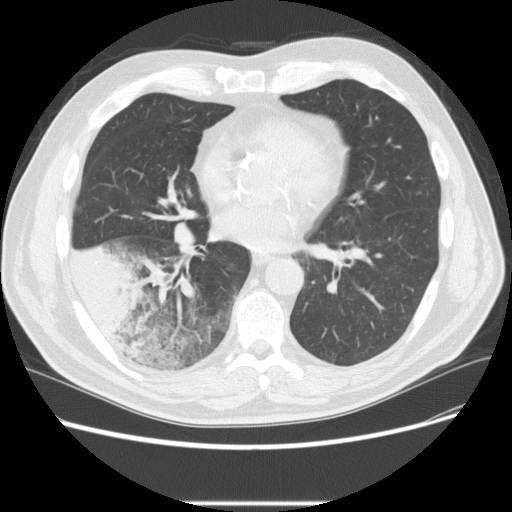
Low-dose screening chest CT, one axial slice; position 102 of 233 along the scan axis; reconstruction kernel STANDARD; lung window (W 1500 / L -600 HU); 2.5 mm slice thickness; 512 × 512 image matrix, field of view 380 × 380 mm.
Annotated regions visible in this slice (manually delineated by an expert):
- lesion 3 (tumor, lower lobe of right lung): box from (x=69, y=242) to (x=141, y=342) px